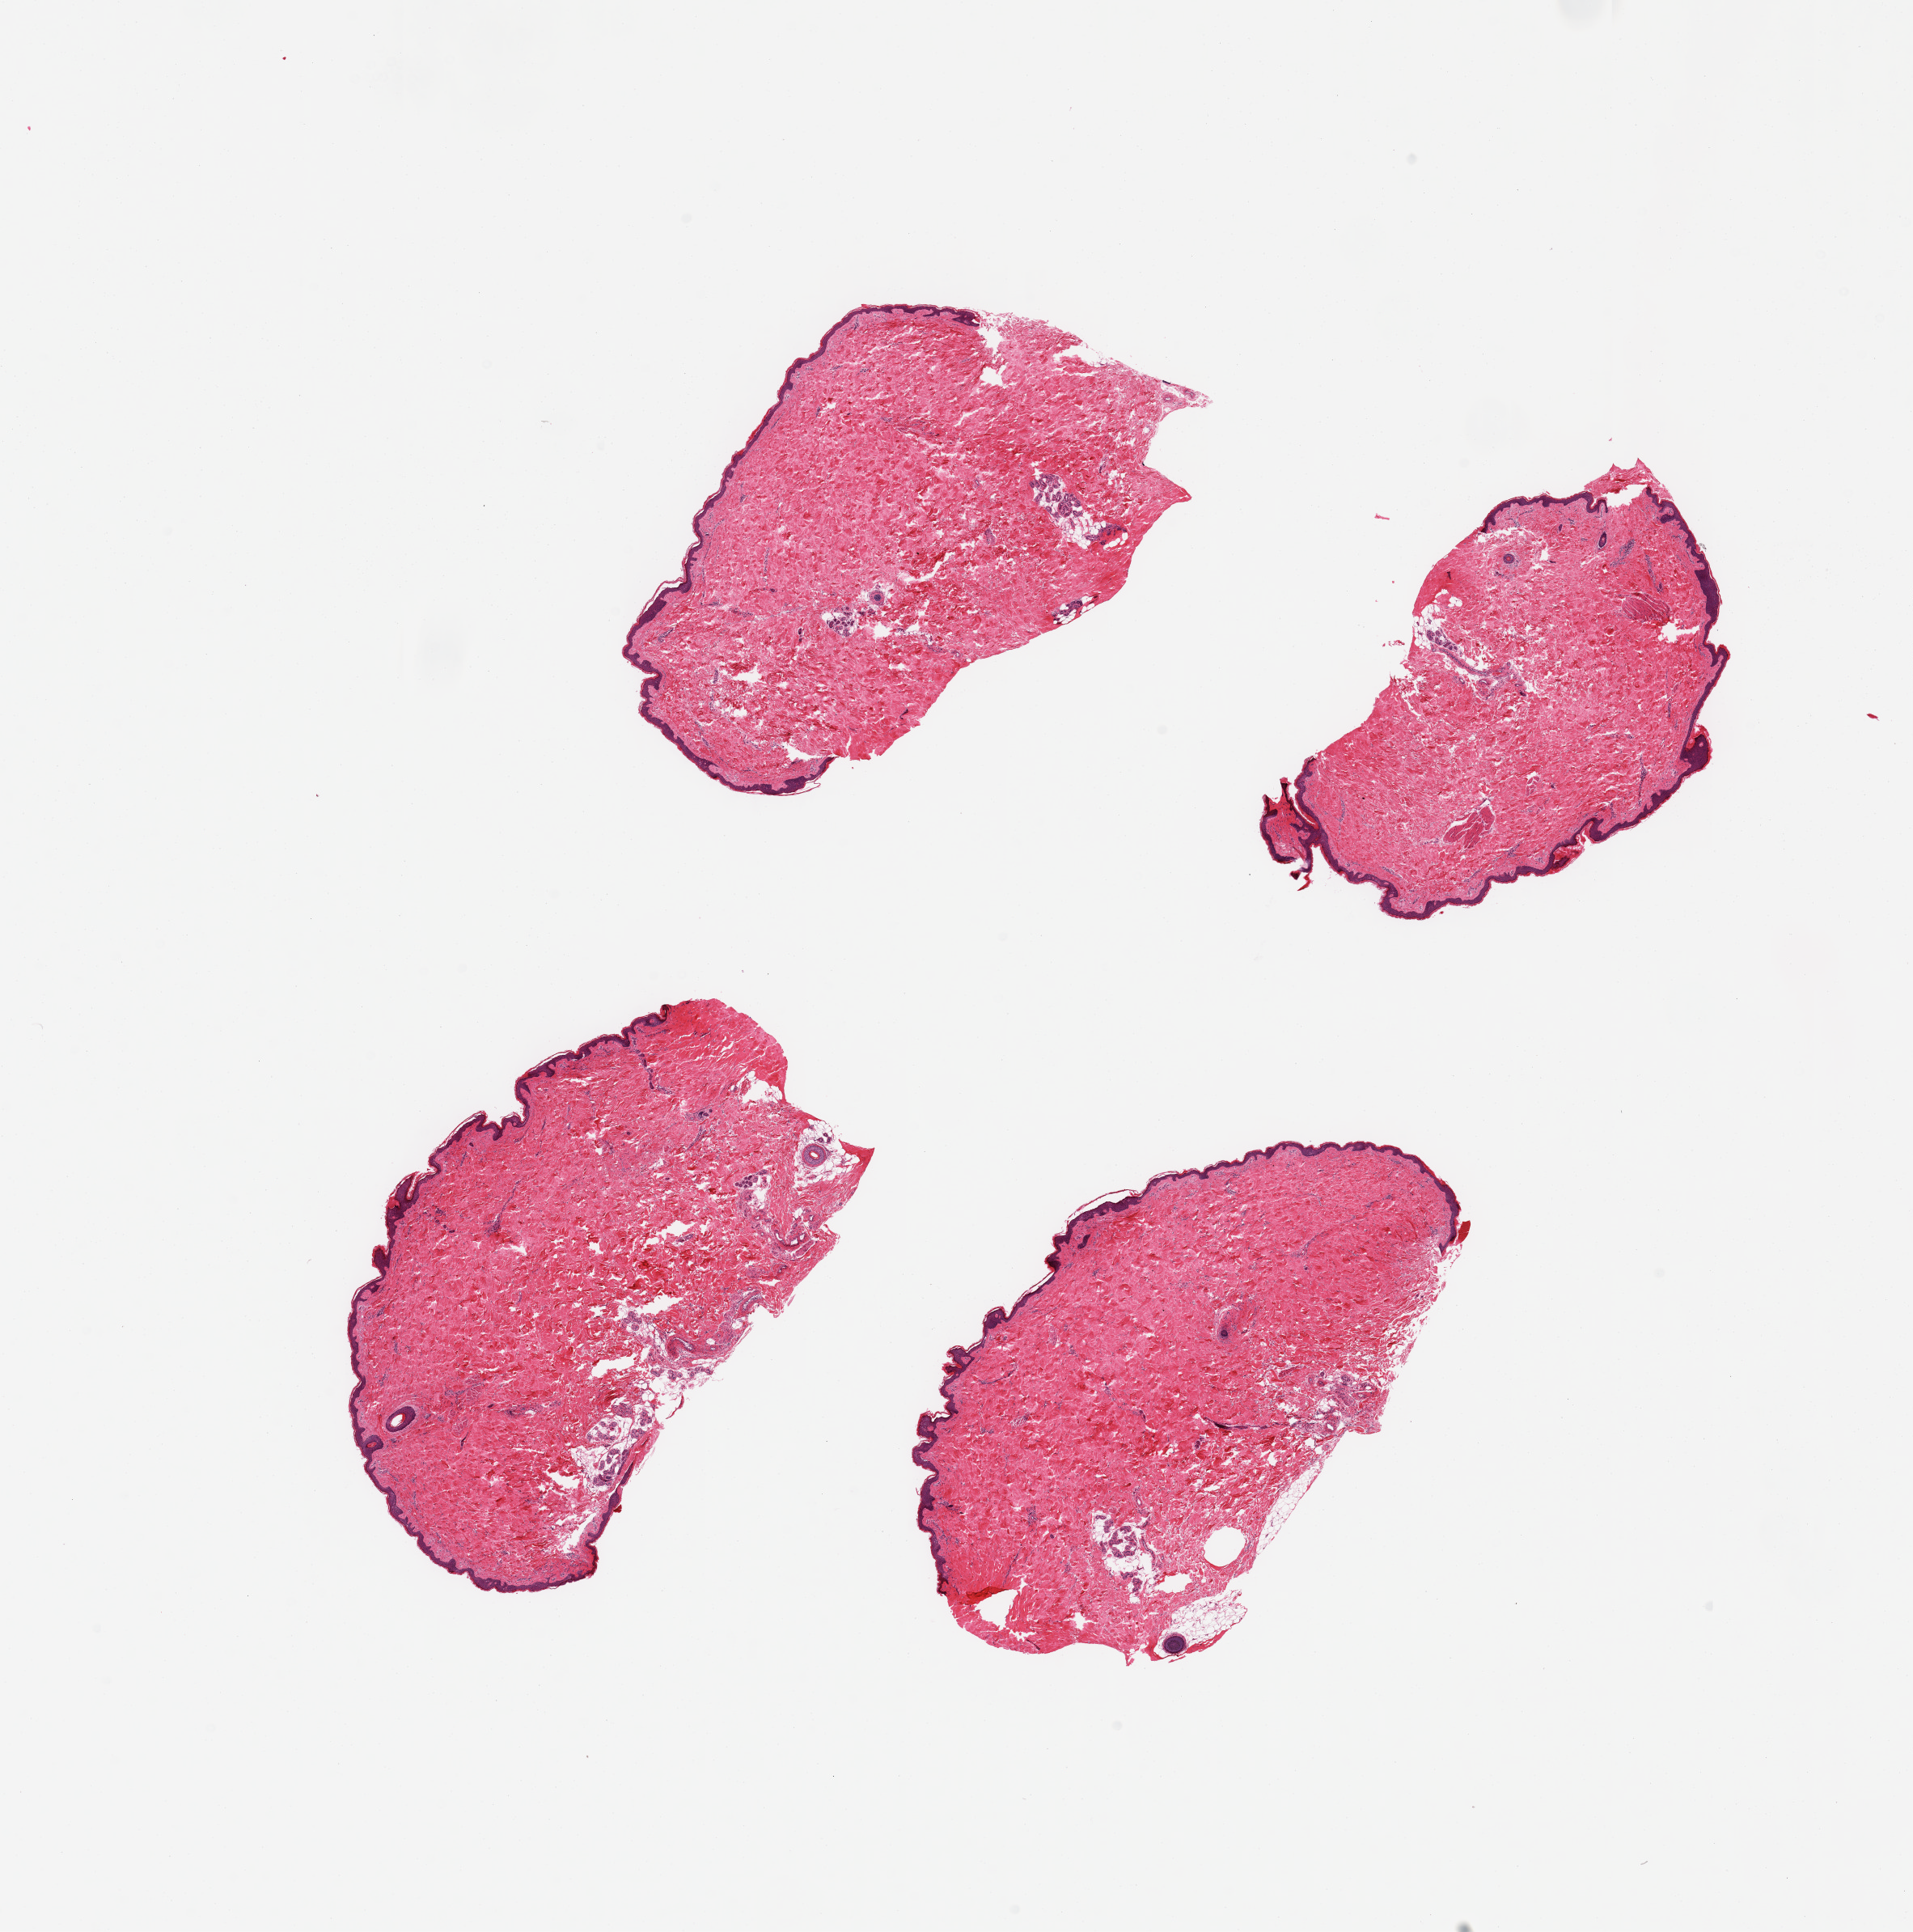
H&E whole-slide image, whole scanned area (about 18.7 x 18.9 mm, slide scanned at 20x) shown as a low-resolution overview. PAXgene-fixed paraffin-embedded (PFPE) section. Sampled site (target tissue): skin of suprapubic region. Donor tissue sample. Donor sex: female.
Review note (as recorded): 4 pieces; well trimmed; dermal fat 5%.